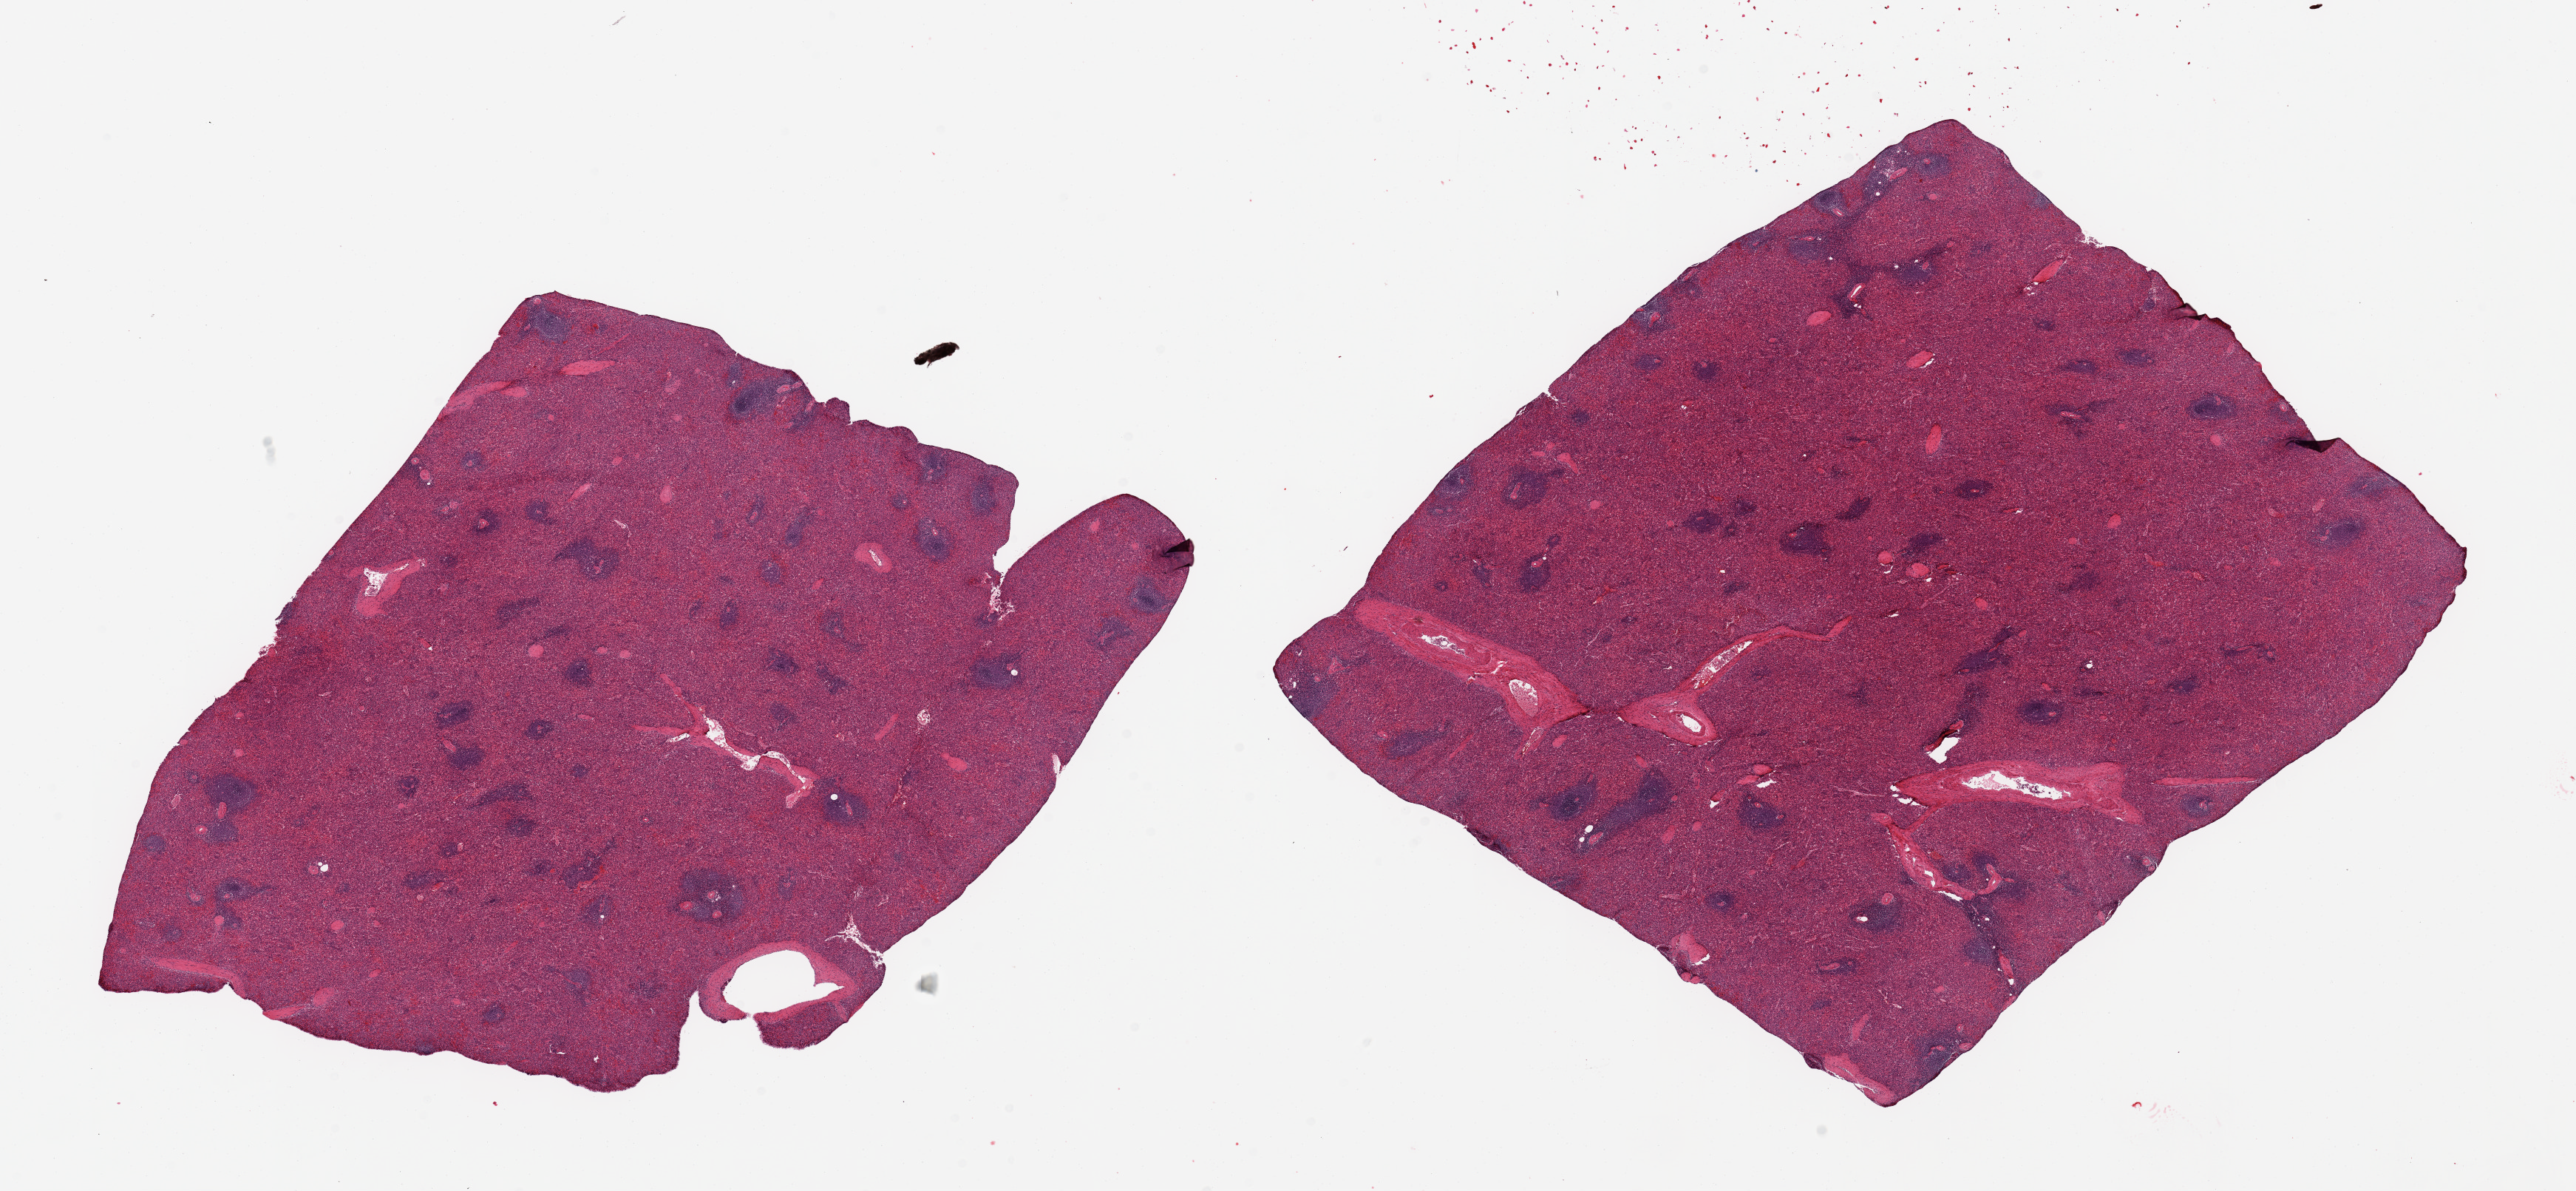
Digitized H&E-stained section, brightfield — shown as a low-resolution overview of the whole scanned area (about 27.6 x 12.7 mm, acquisition: 20x scan), PAXgene-fixed paraffin-embedded (PFPE) section, target tissue: spleen, tissue donor sample. Donor sex: male.
Review note (as recorded): 2 pieces; mild congestion.